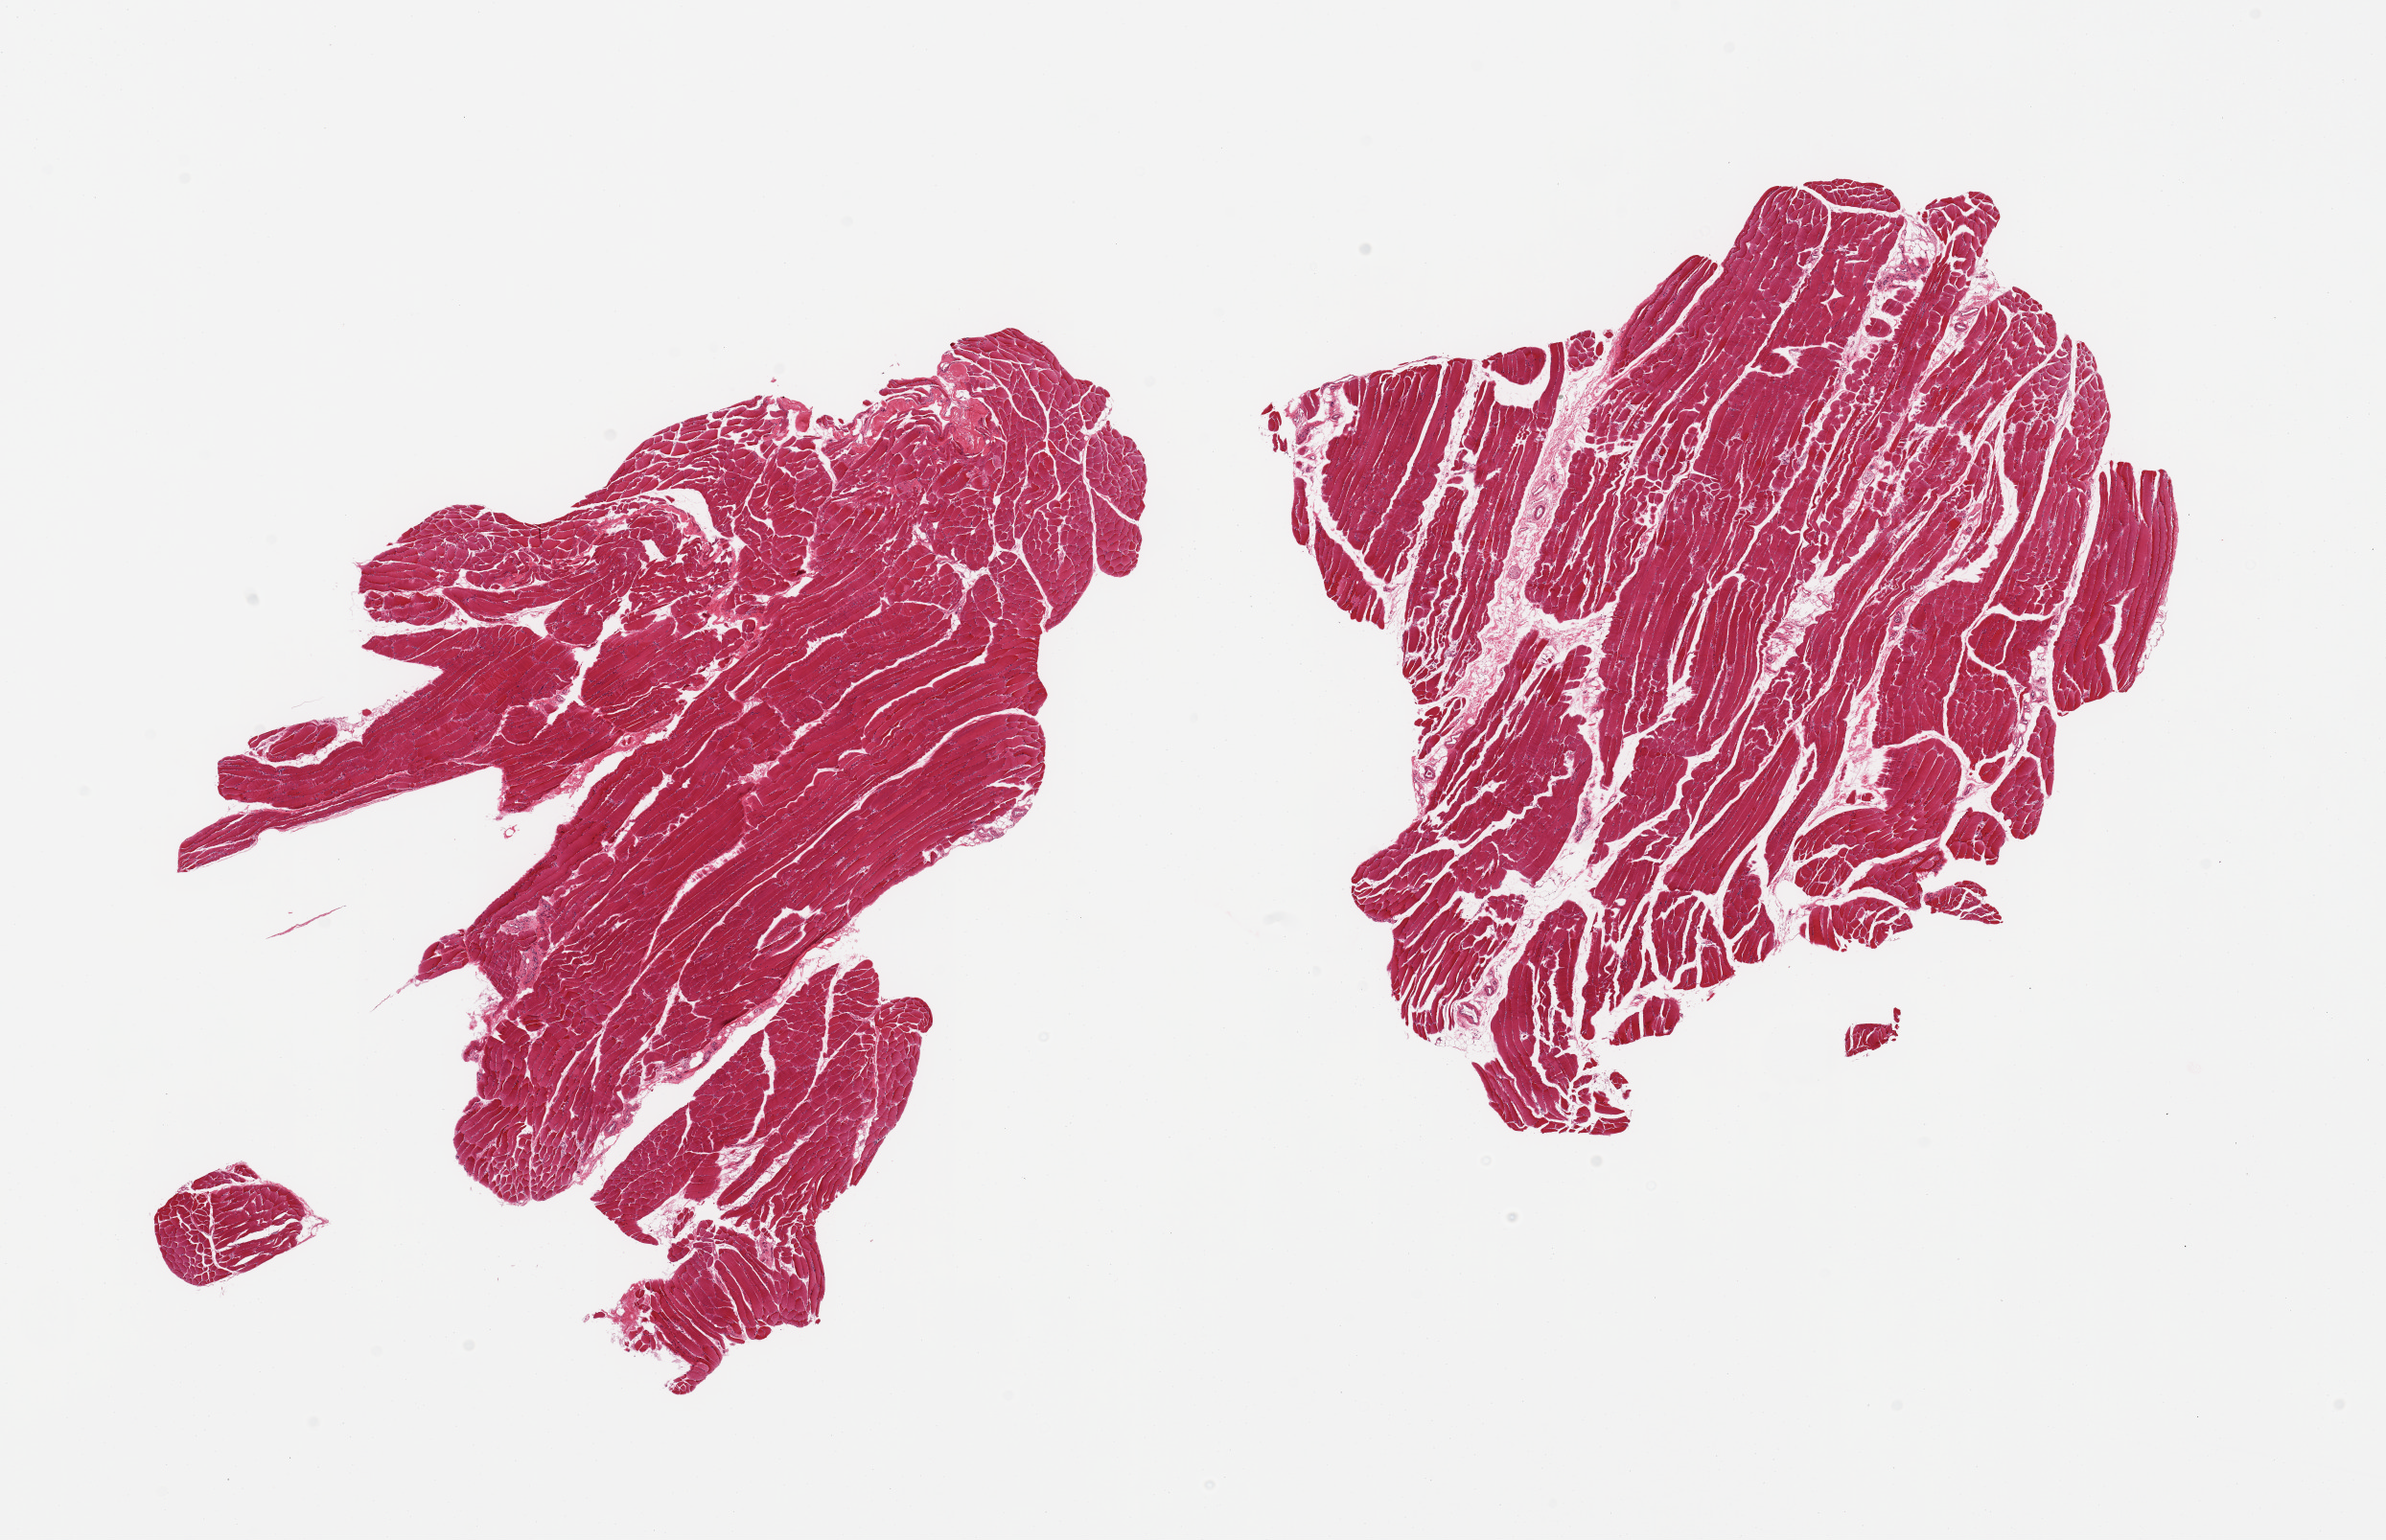
Digitized haematoxylin and eosin-stained section, a low-resolution overview of the entire scanned area, about 19.7 x 12.7 mm (acquisition: 20x scan), PAXgene-fixed, paraffin-embedded tissue, target tissue: skeletal muscle, tissue donor sample.
Pathologist's review note for this sample: 2 pieces.